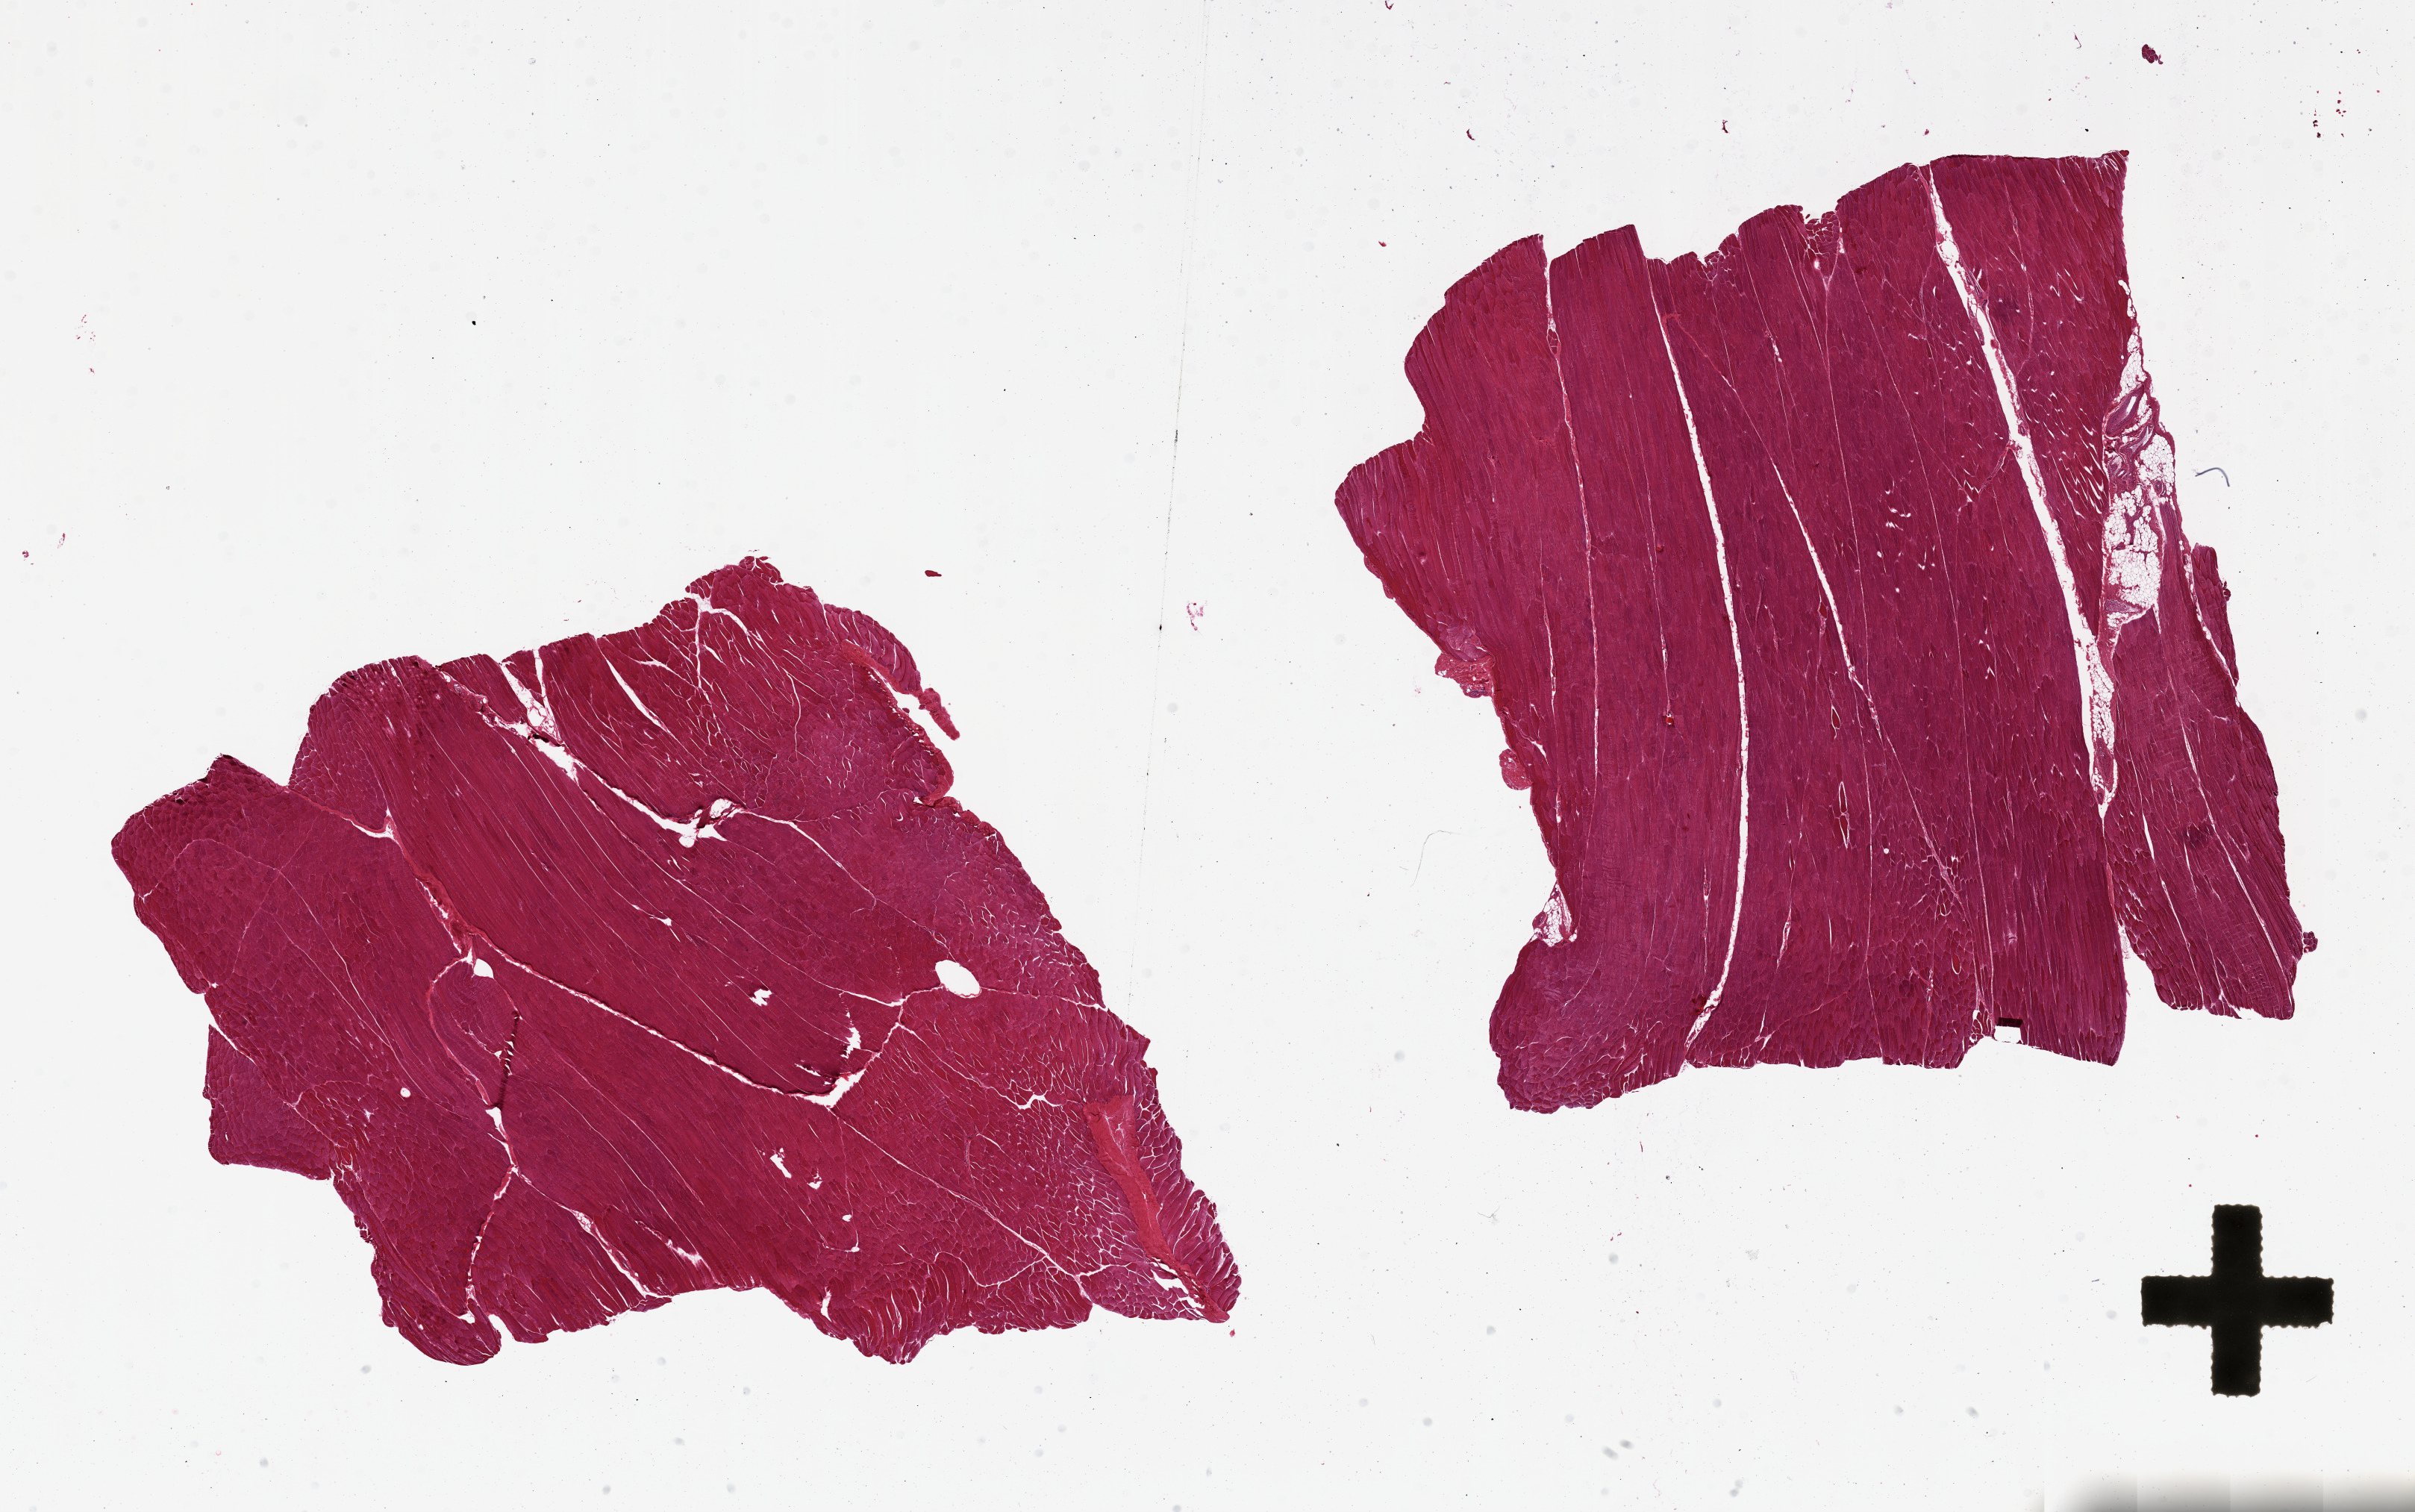
Haematoxylin and eosin whole-slide image, whole scanned area (about 25.6 x 16.0 mm) shown as a low-resolution overview. PAXgene-fixed paraffin-embedded (PFPE) section. Sampled site (target tissue): skeletal muscle. Tissue donor sample. Donor: male.
- pathologist's review note for this sample: 2 pieces, 1 with 5% internal fat